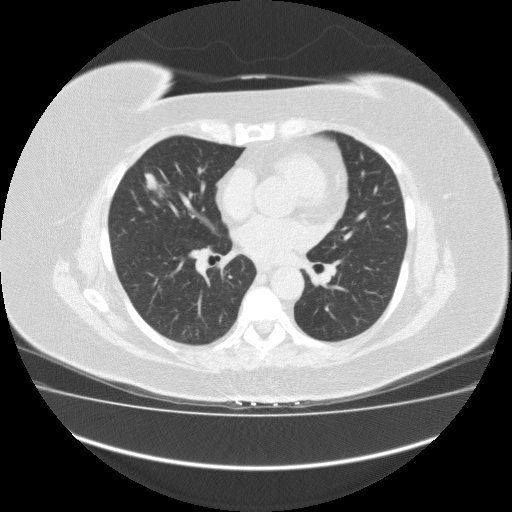
Low-dose screening chest CT, one axial slice. Position 84 of 162 along the scan axis. Reconstruction kernel FC10. 120 kVp. Lung window (W 1500 / L -600 HU). 2 mm slice thickness. 512 × 512 image matrix, field of view 420 × 420 mm.
Annotated regions visible in this slice (expert manual segmentation):
- lesion 1 (tumor, middle lobe of right lung): bounding box <145,173,159,190> (left, top, right, bottom; pixels)